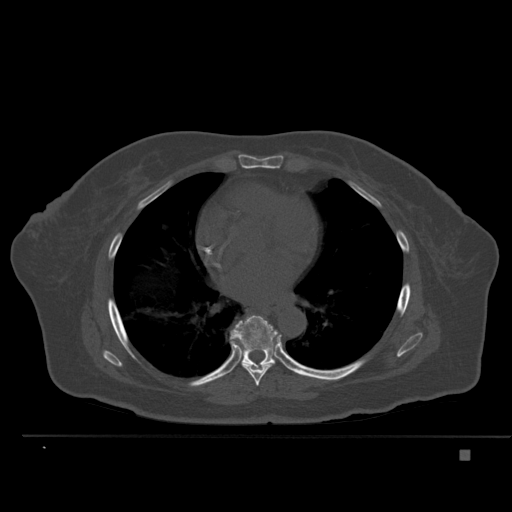
CT including the spine, one axial slice; slice 319 of 477 in the series (ordered by position); bone window (W 1800 / L 400 HU); 1.5 mm slice thickness; 512 × 512 image matrix, field of view 422 × 422 mm. Female patient, age 74 years. Case-level facts recorded for this patient, not image findings: primary cancer: colon.
Annotated regions visible in this slice (semi-automatically segmented with operator editing):
- T7 vertebra: box from (x=231, y=338) to (x=276, y=386) px
- T8 vertebra: (x=230, y=315)–(x=278, y=369)